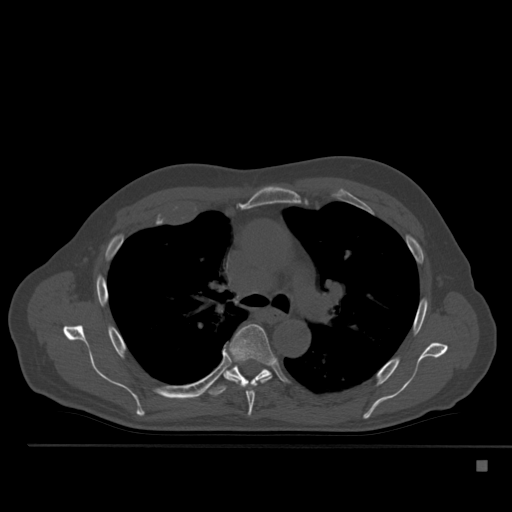
CT including the spine, one axial slice; slice 358 of 517 in the series (ordered by position); reconstruction kernel Br40s; bone window (W 1800 / L 400 HU); 512 × 512 image matrix. Patient: male, 70 years. Case-level facts recorded for this patient, not image findings: primary cancer: renal; vertebrae with lytic lesions (as recorded): T4, T6, T10, T12, L3, L4, L5.
Annotated regions visible in this slice (semi-automatically segmented with operator editing):
- T5 vertebra: bounding box <222,324,275,416> (left, top, right, bottom; pixels)
- T6 vertebra: <205,364,271,396>